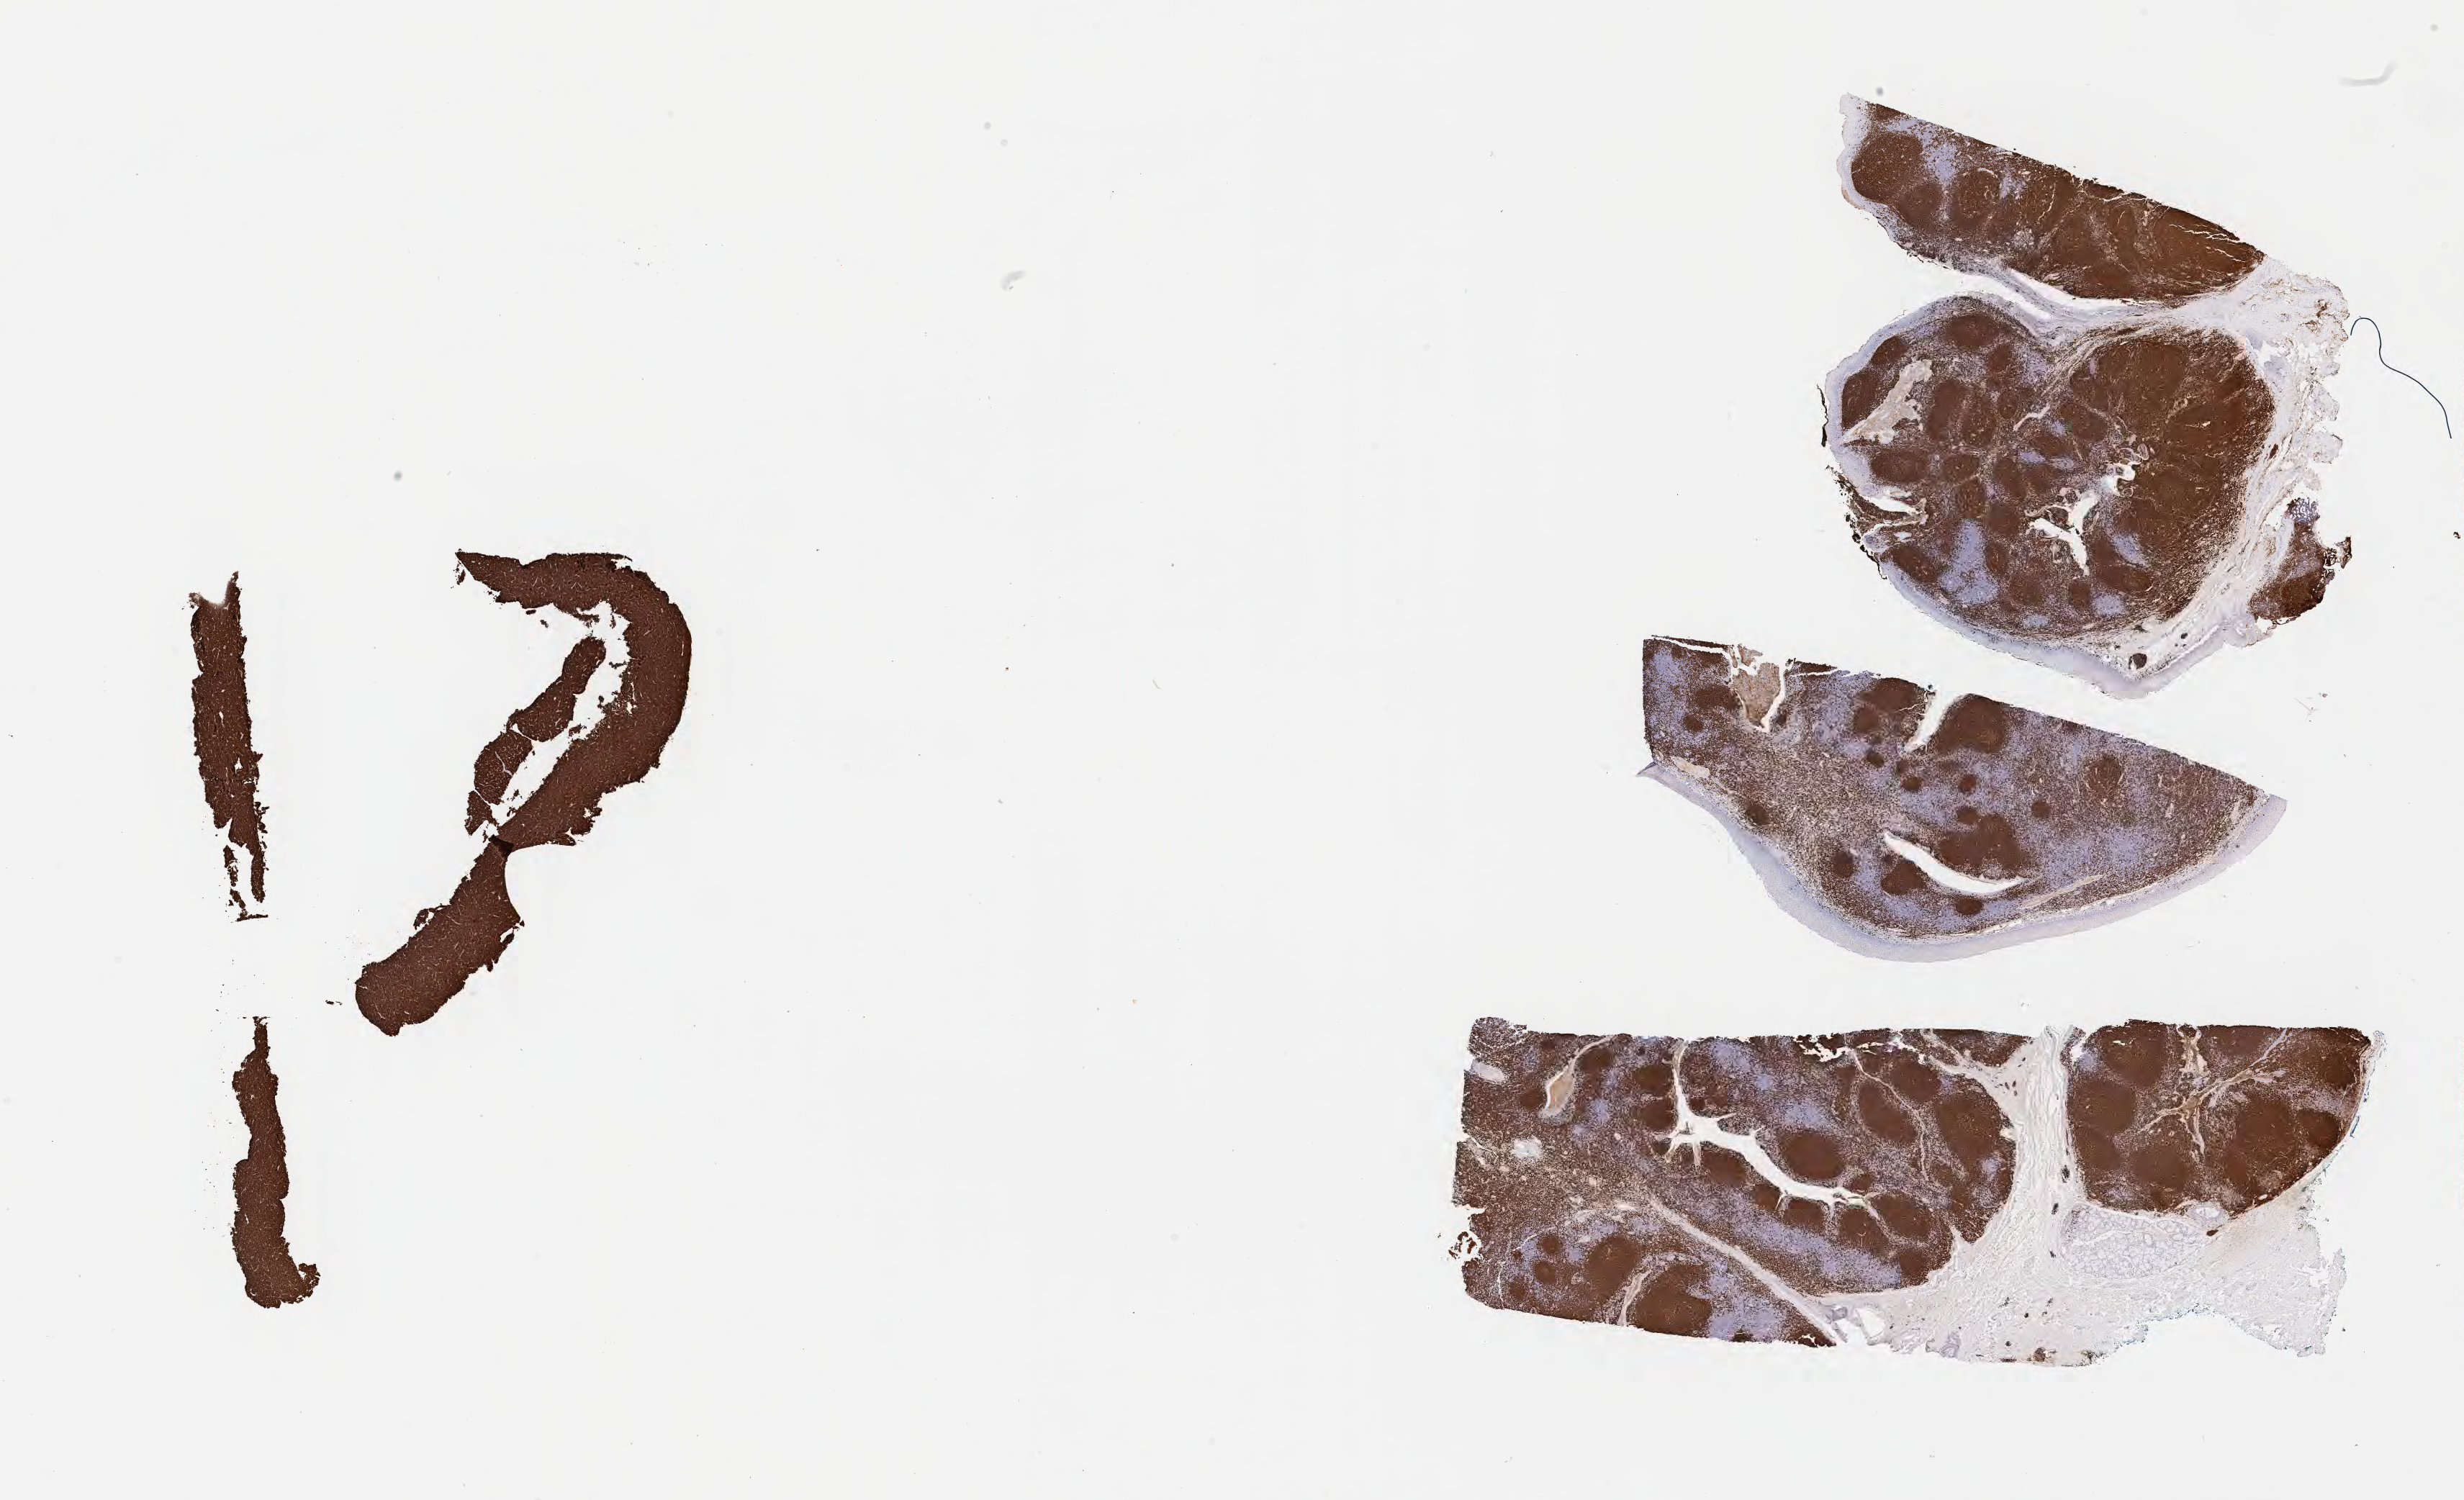
IHC for CD20, whole-slide image, a low-resolution overview of the entire scanned area, about 27.7 x 16.8 mm. Tumor tissue. Anatomic site: peritoneum. Female, age 7 years at initial diagnosis.
Histologic diagnosis: Burkitt lymphoma, NOS.